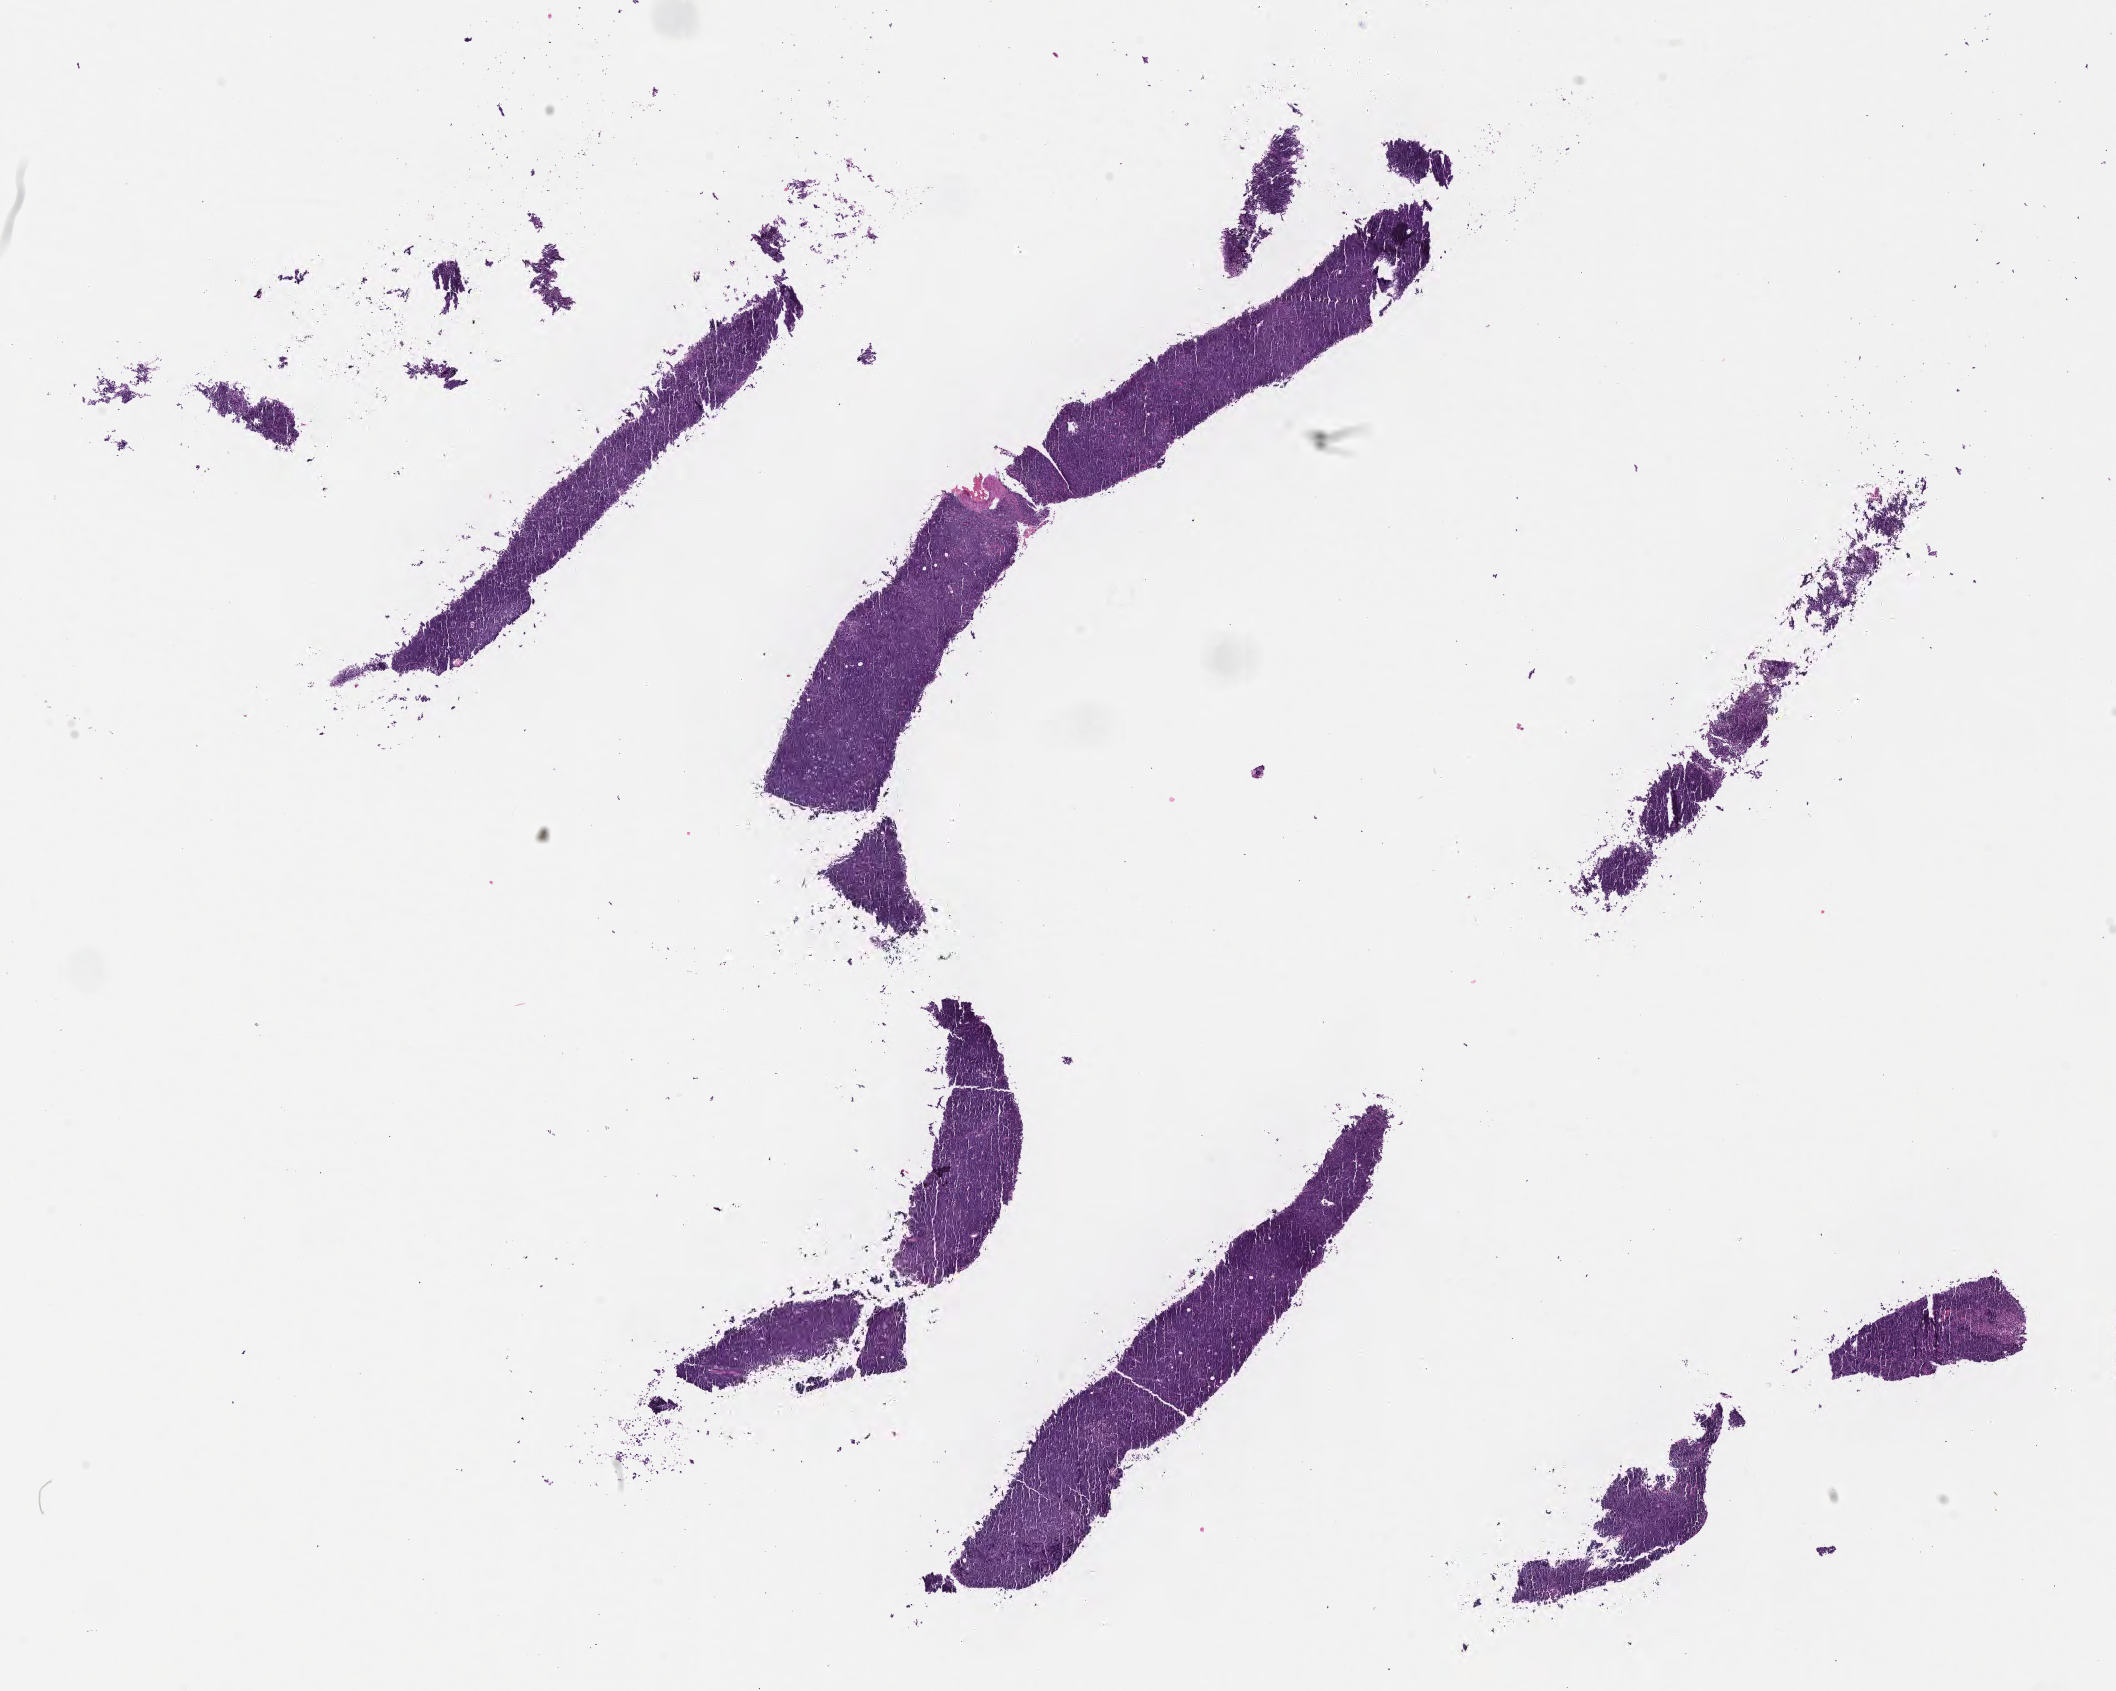
Whole-slide image, haematoxylin and eosin stain, low-resolution overview of the scanned area, about 17.1 x 13.7 mm, FFPE section, specimen: primary tumor. Patient: male, 29 years old. Composition of this section per pathologist review: tumor cells 95%, tumor nuclei 95%, stromal cells 0%, necrosis 5%, normal cells 0%. Infiltration values recorded for this section: lymphocyte infiltration 50%, monocyte infiltration 25%, neutrophil infiltration 5%.
* Ann Arbor stage (patient): Stage IV
* diagnosis: Burkitt lymphoma, NOS